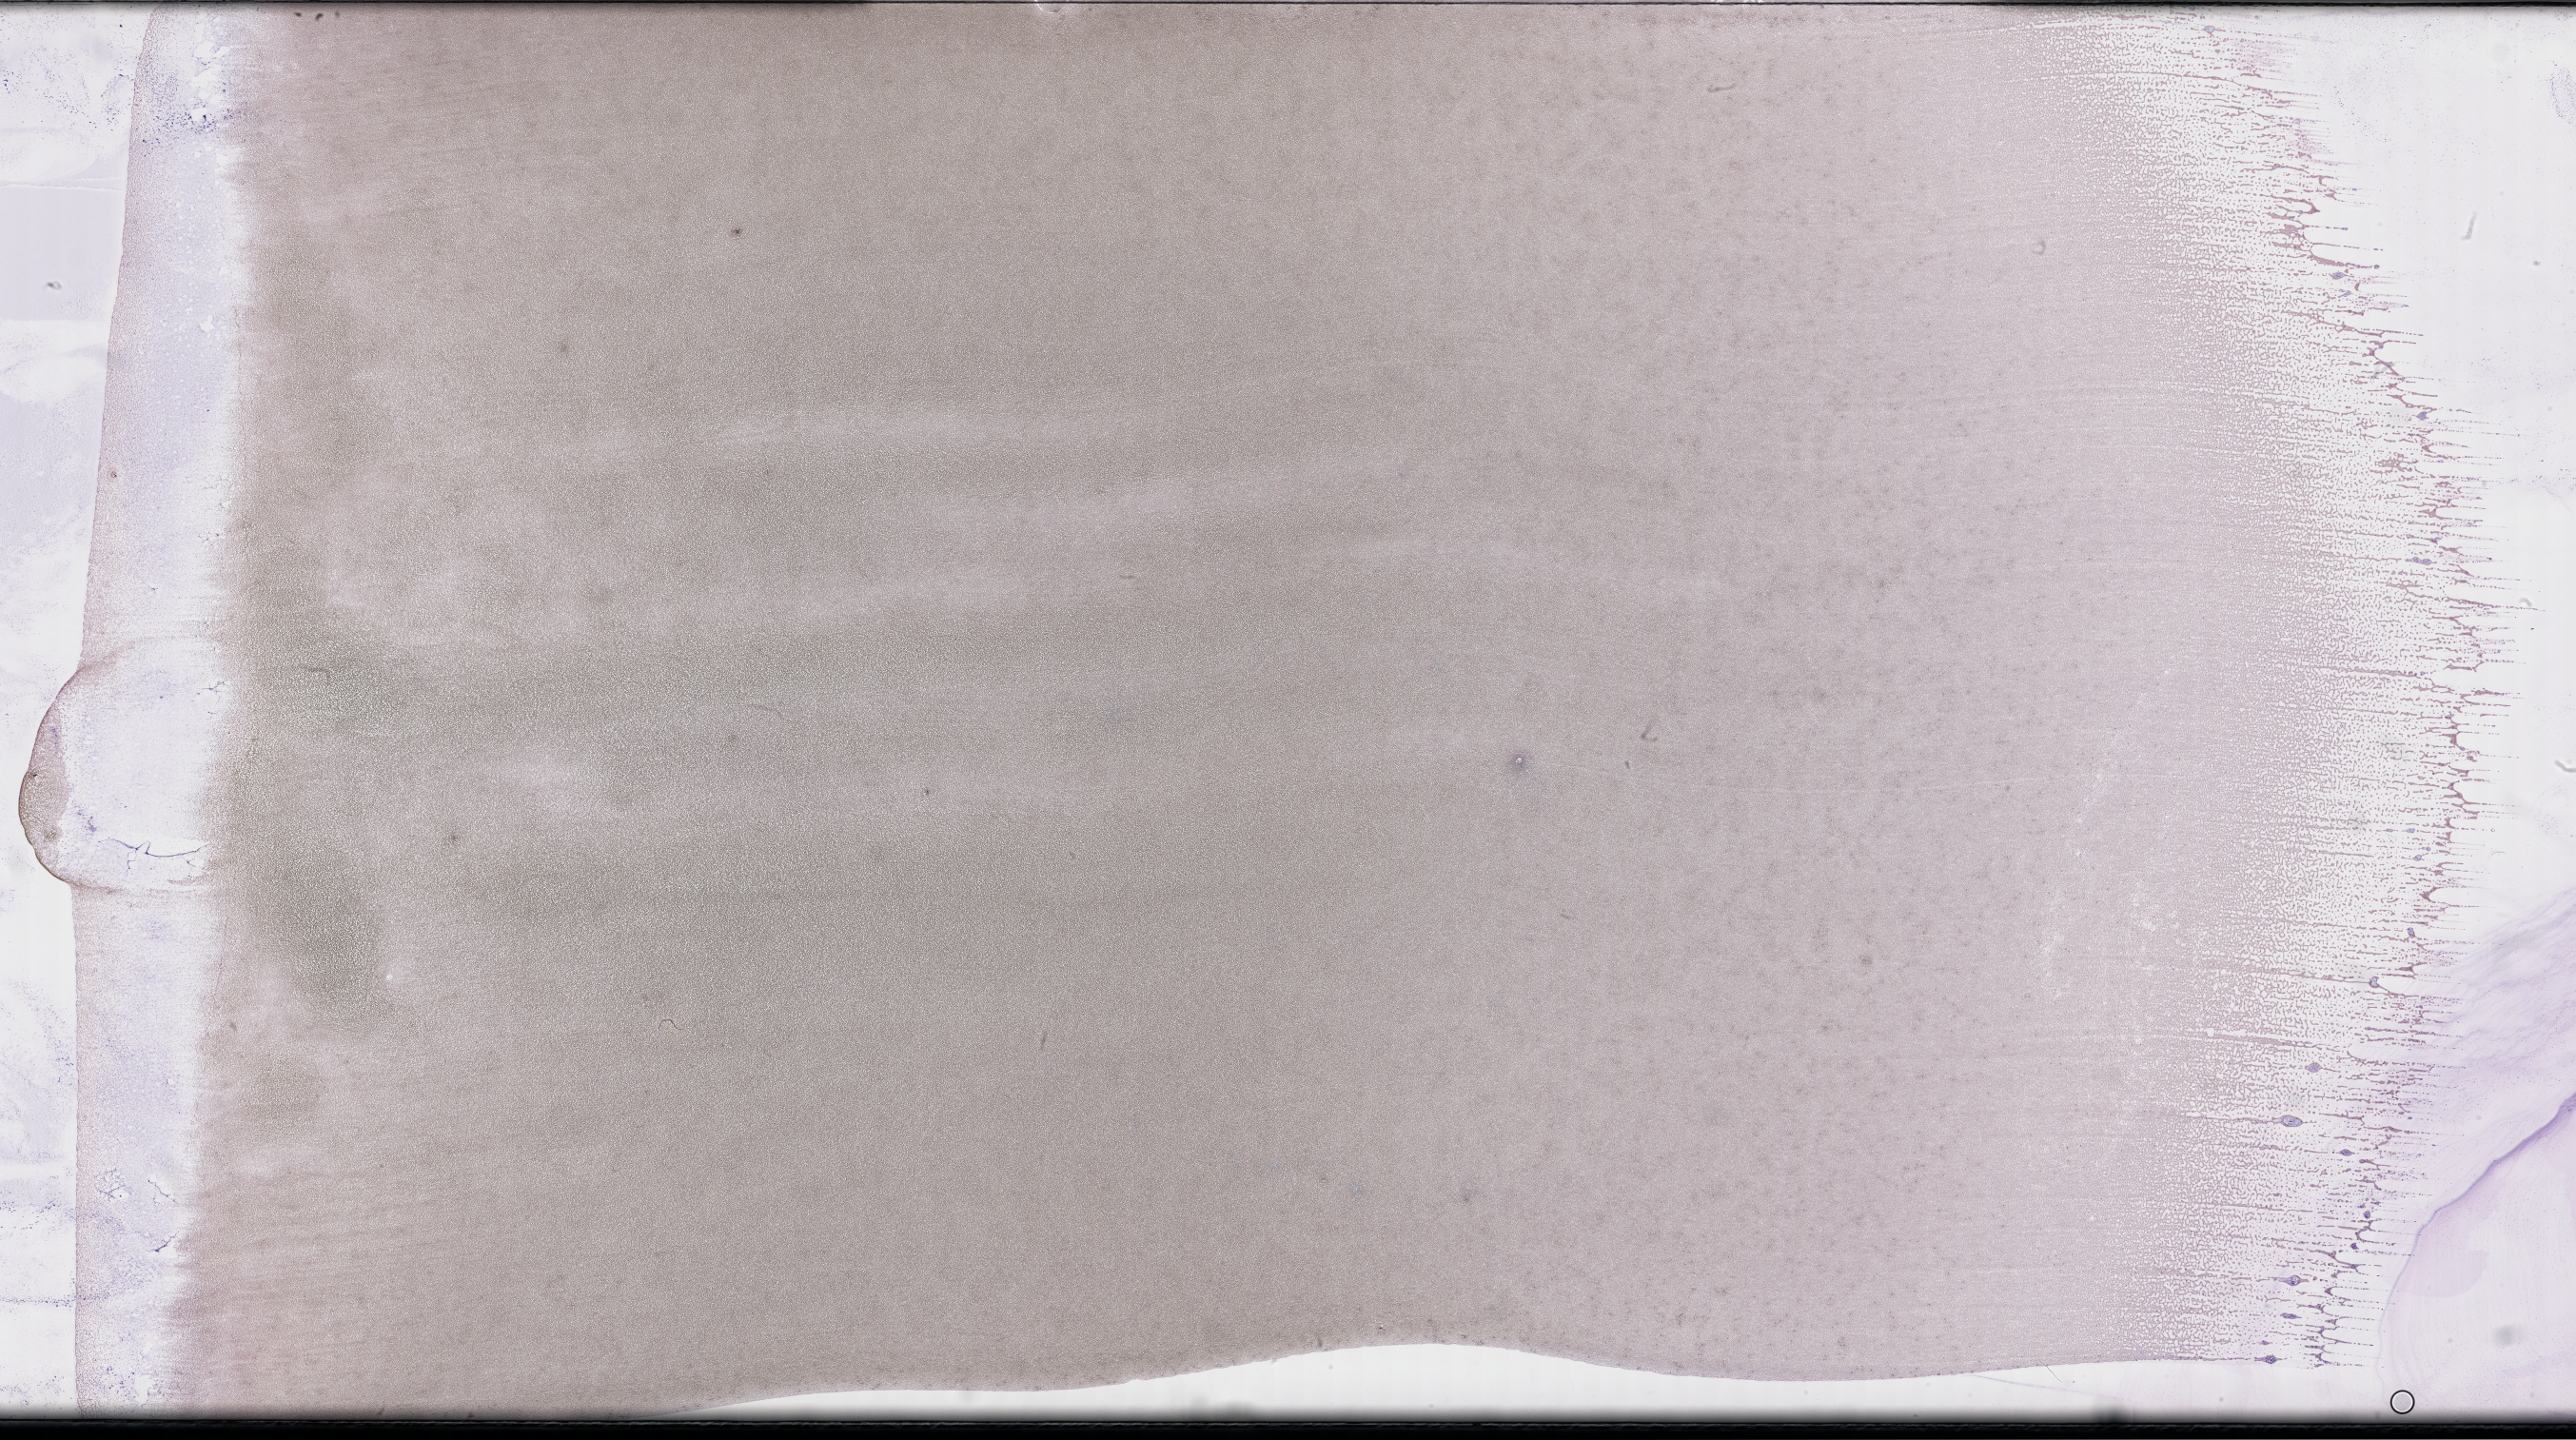
Whole-slide image of a whole blood smear, Wright-Giemsa stain — low-resolution overview of the scanned area, about 43.7 x 24.4 mm; smear from an EDTA sample. Patient: male.
• patient diagnosis: Plasma Cell Myeloma